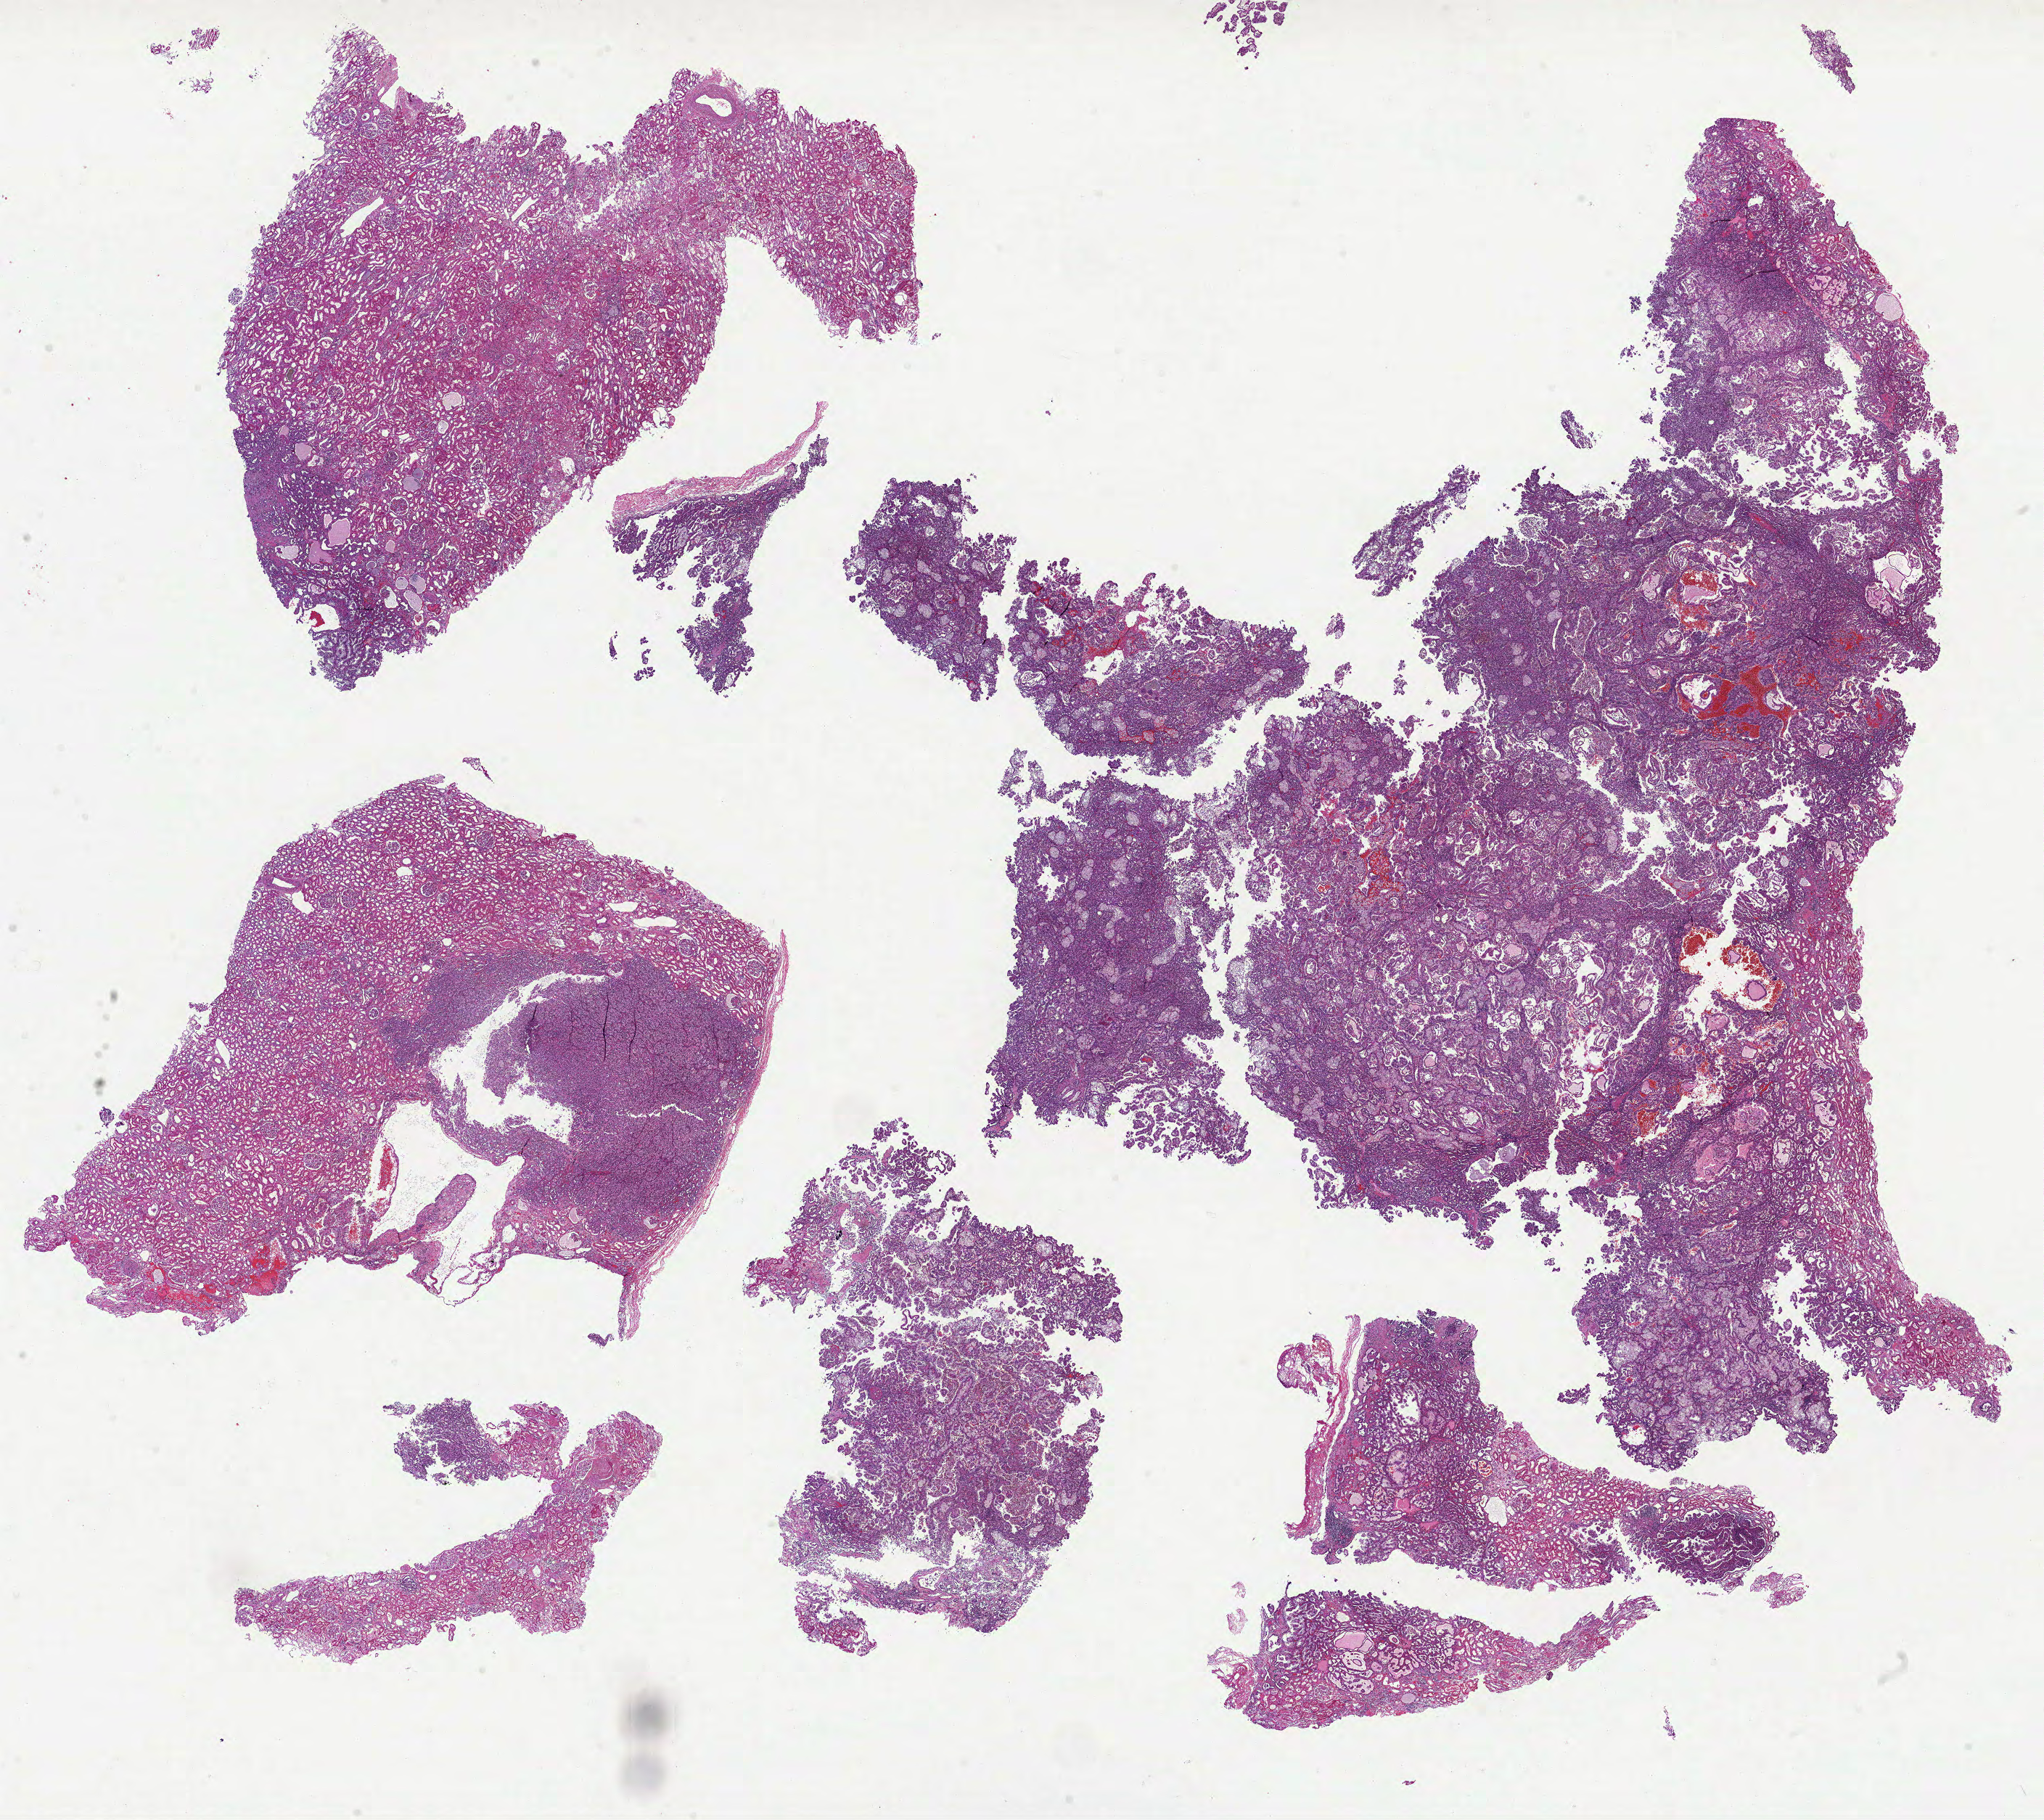
Whole-slide histology image, H&E-stained, whole scanned area (about 22.7 x 20.2 mm, slide scanned at 40x) shown as a low-resolution overview. Formalin-fixed paraffin-embedded (FFPE) diagnostic section. Kidney, primary tumour sample. Male patient; age at initial diagnosis 53 years.
* pathologic diagnosis: Papillary adenocarcinoma, NOS
* AJCC pathologic stage: I